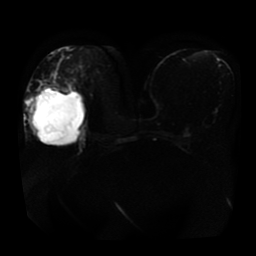
Breast MRI, one axial slice. Position 22 of 41 along the scan axis. Diffusion-weighted series; image 2 of 4 stored at this slice position (different b-values; order by instance number). 1.5 T. 5 mm slice thickness. 256 × 256 image matrix, field of view 360 × 360 mm. Female patient.
Annotated regions visible in this slice (outlined manually by an expert reader):
- tumour on diffusion-weighted imaging: box from (x=27, y=102) to (x=39, y=136) px